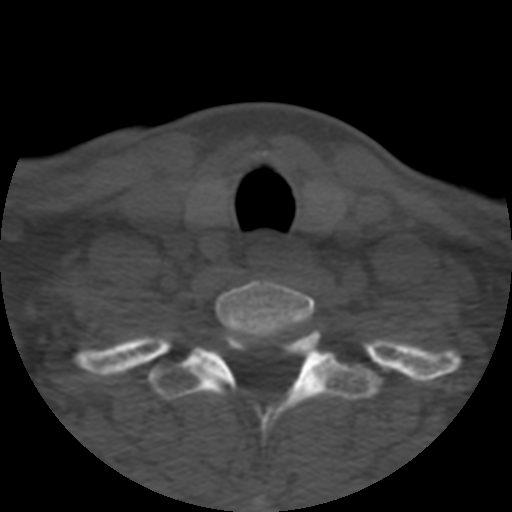
CT including the spine, one axial slice; position 454 of 508 along the scan axis; 120 kVp; bone window (W 1800 / L 400 HU); 1.25 mm slice thickness; 512 × 512 image matrix, field of view 160 × 160 mm. Patient age 57 years. From the clinical record (not read from this slice): primary cancer: prostate.
Structures marked on this image (semi-automatic segmentation, software-assisted and operator-edited):
- T1 vertebra: bounding box (x1, y1, x2, y2) in pixels: (93, 333, 380, 508)